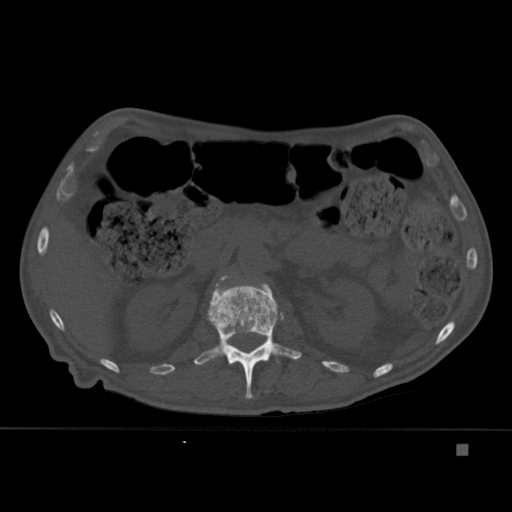
CT including the spine, one axial slice; position 180 of 451 along the scan axis; bone window (W 1800 / L 400 HU); 1.5 mm slice thickness; 512 × 512 image matrix. Male patient, age 75 years. Case-level facts recorded for this patient, not image findings: primary cancer: prostate.
Outlined on this slice (semi-automatic segmentation, software-assisted and operator-edited):
- L1 vertebra: box from (x=194, y=283) to (x=302, y=399) px
- L2 vertebra: (x=220, y=275)–(x=230, y=281)